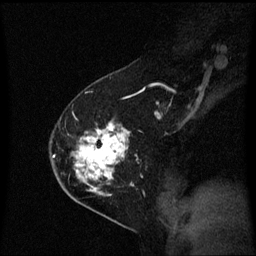
Breast MRI (dynamic contrast-enhanced), one sagittal slice. Slice 38 of 60 in the series (ordered by position). Dynamic contrast-enhanced series, image 2 of 3 at this slice position (ordered by acquisition). 1.5 T. TE 4.2 ms, TR 8.4 ms. 2 mm slice thickness. 256 × 256 image matrix, field of view 210 × 210 mm. Female patient, age 54 years. Case-level facts recorded for this patient, not image findings: setting: breast cancer imaged before/during neoadjuvant chemotherapy; receptor status: HER2-positive.
Structures marked on this image (semi-automatic segmentation, software-assisted and operator-edited):
- analysis volume of interest (the breast-tissue region the enhancement analysis was run in; not a lesion): bounding box (x1, y1, x2, y2) in pixels: (59, 120, 136, 199)
- tumour enhancement mask (voxels above the 70 % enhancement threshold inside the analysis volume of interest): (76, 125, 129, 193)